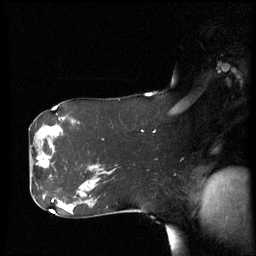
Breast MRI (dynamic contrast-enhanced), one sagittal slice. Slice 37 of 60 in the series (ordered by position). Dynamic contrast-enhanced series, image 2 of 3 at this slice position (ordered by acquisition). 1.5 T. TE 4.2 ms, TR 8.4 ms. 2.9 mm slice thickness. 256 × 256 image matrix. Patient: female, 61 years. Case-level facts recorded for this patient, not image findings: setting: breast cancer imaged before/during neoadjuvant chemotherapy; receptor status: HR-positive, HER2-negative.
Annotated regions visible in this slice (semi-automatic segmentation, software-assisted and operator-edited):
- analysis volume of interest (the breast-tissue region the enhancement analysis was run in; not a lesion): bounding box (x1, y1, x2, y2) in pixels: (31, 142, 56, 177)
- tumour enhancement mask (voxels above the 70 % enhancement threshold inside the analysis volume of interest): (39, 158, 50, 167)